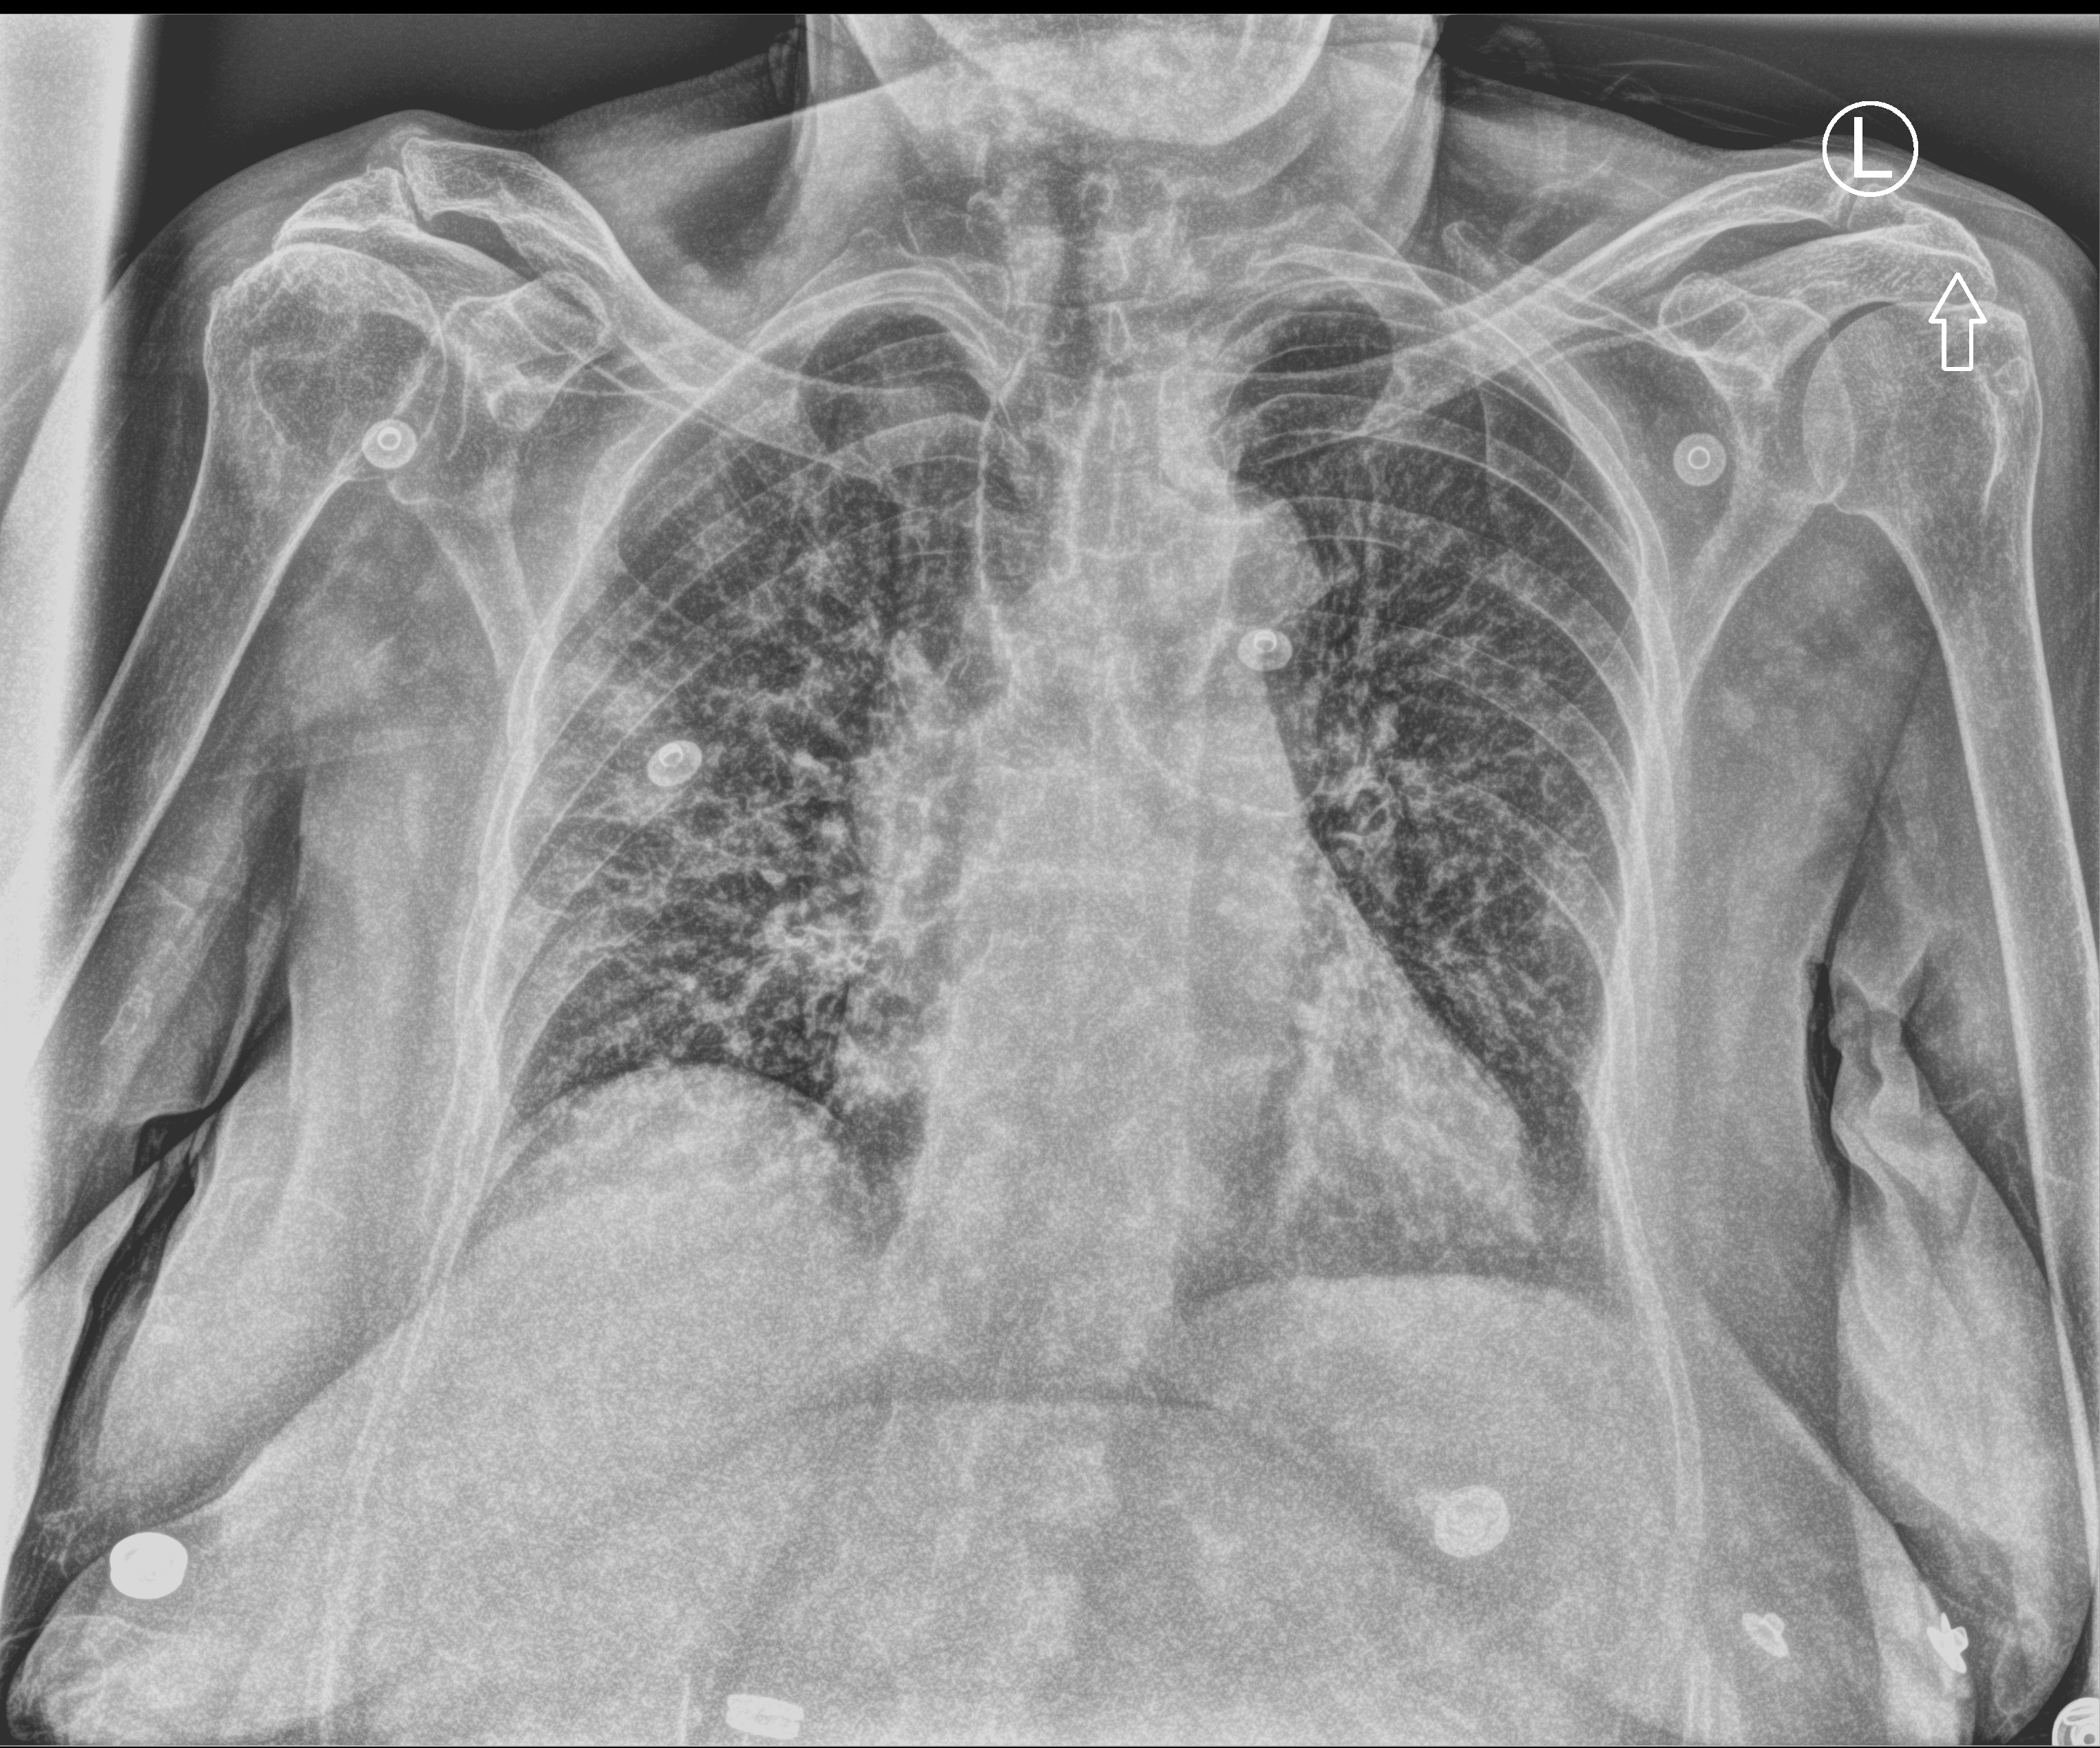
Portable chest radiograph, anteroposterior (AP) projection. Female patient hospitalised with COVID-19, age 75–90 years.
Admission-level facts for this patient (not findings on this image; timing relative to this image not recorded):
- mechanically ventilated during this hospital stay: no